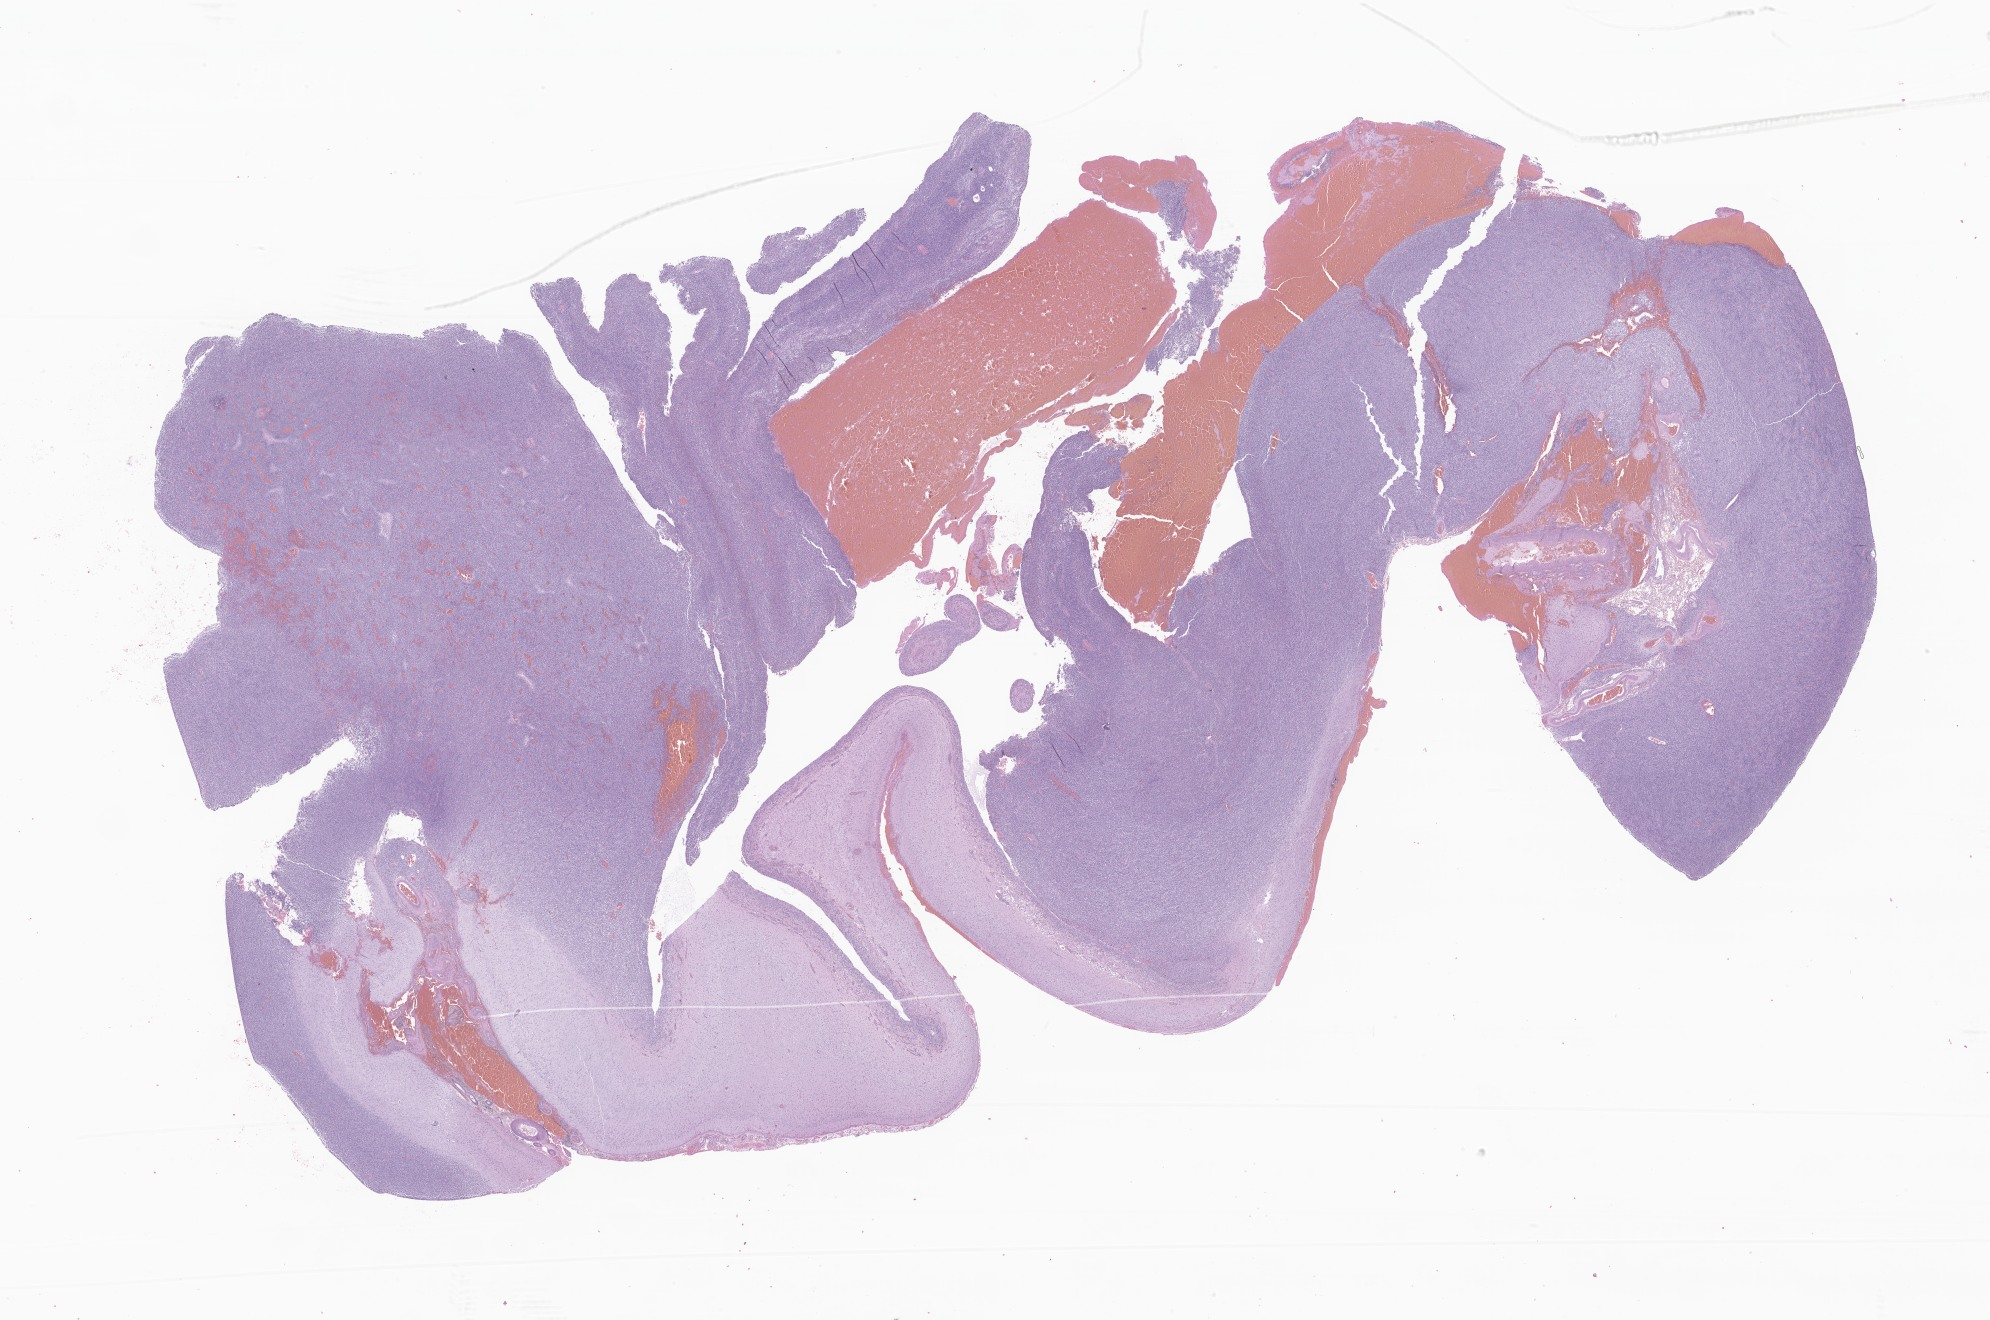
H&E whole-slide image of tumor tissue from the cerebrum, whole scanned area (about 33.6 x 22.3 mm) shown as a low-resolution overview, formalin-fixed paraffin-embedded section. Patient female; age 119 days.
Recorded diagnosis: Neoplasm, malignant.